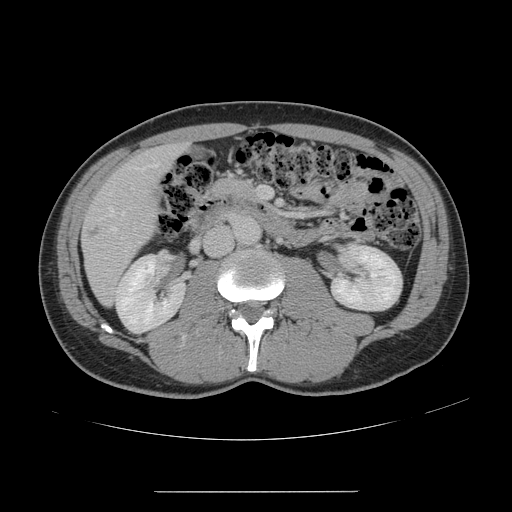
Contrast-enhanced abdominal CT, one axial slice. Position 53 of 178 along the scan axis. Intravenous contrast given. Soft-tissue window (W 400 / L 40 HU). 512 × 512 image matrix. Male patient, age 53 years. From the clinical record (not read from this slice): diagnosis: colorectal cancer liver metastases, imaged before liver resection; multiple liver metastases: yes; largest metastasis: 2.4 cm.
Annotated regions visible in this slice (outlined manually by an expert reader):
- hepatic veins: bounding box [x1, y1, x2, y2] px = [99, 164, 158, 233]
- liver: [83, 146, 180, 303]
- portal vein (with intrahepatic branches): [259, 186, 267, 199]
- liver metastasis: [89, 228, 100, 237]